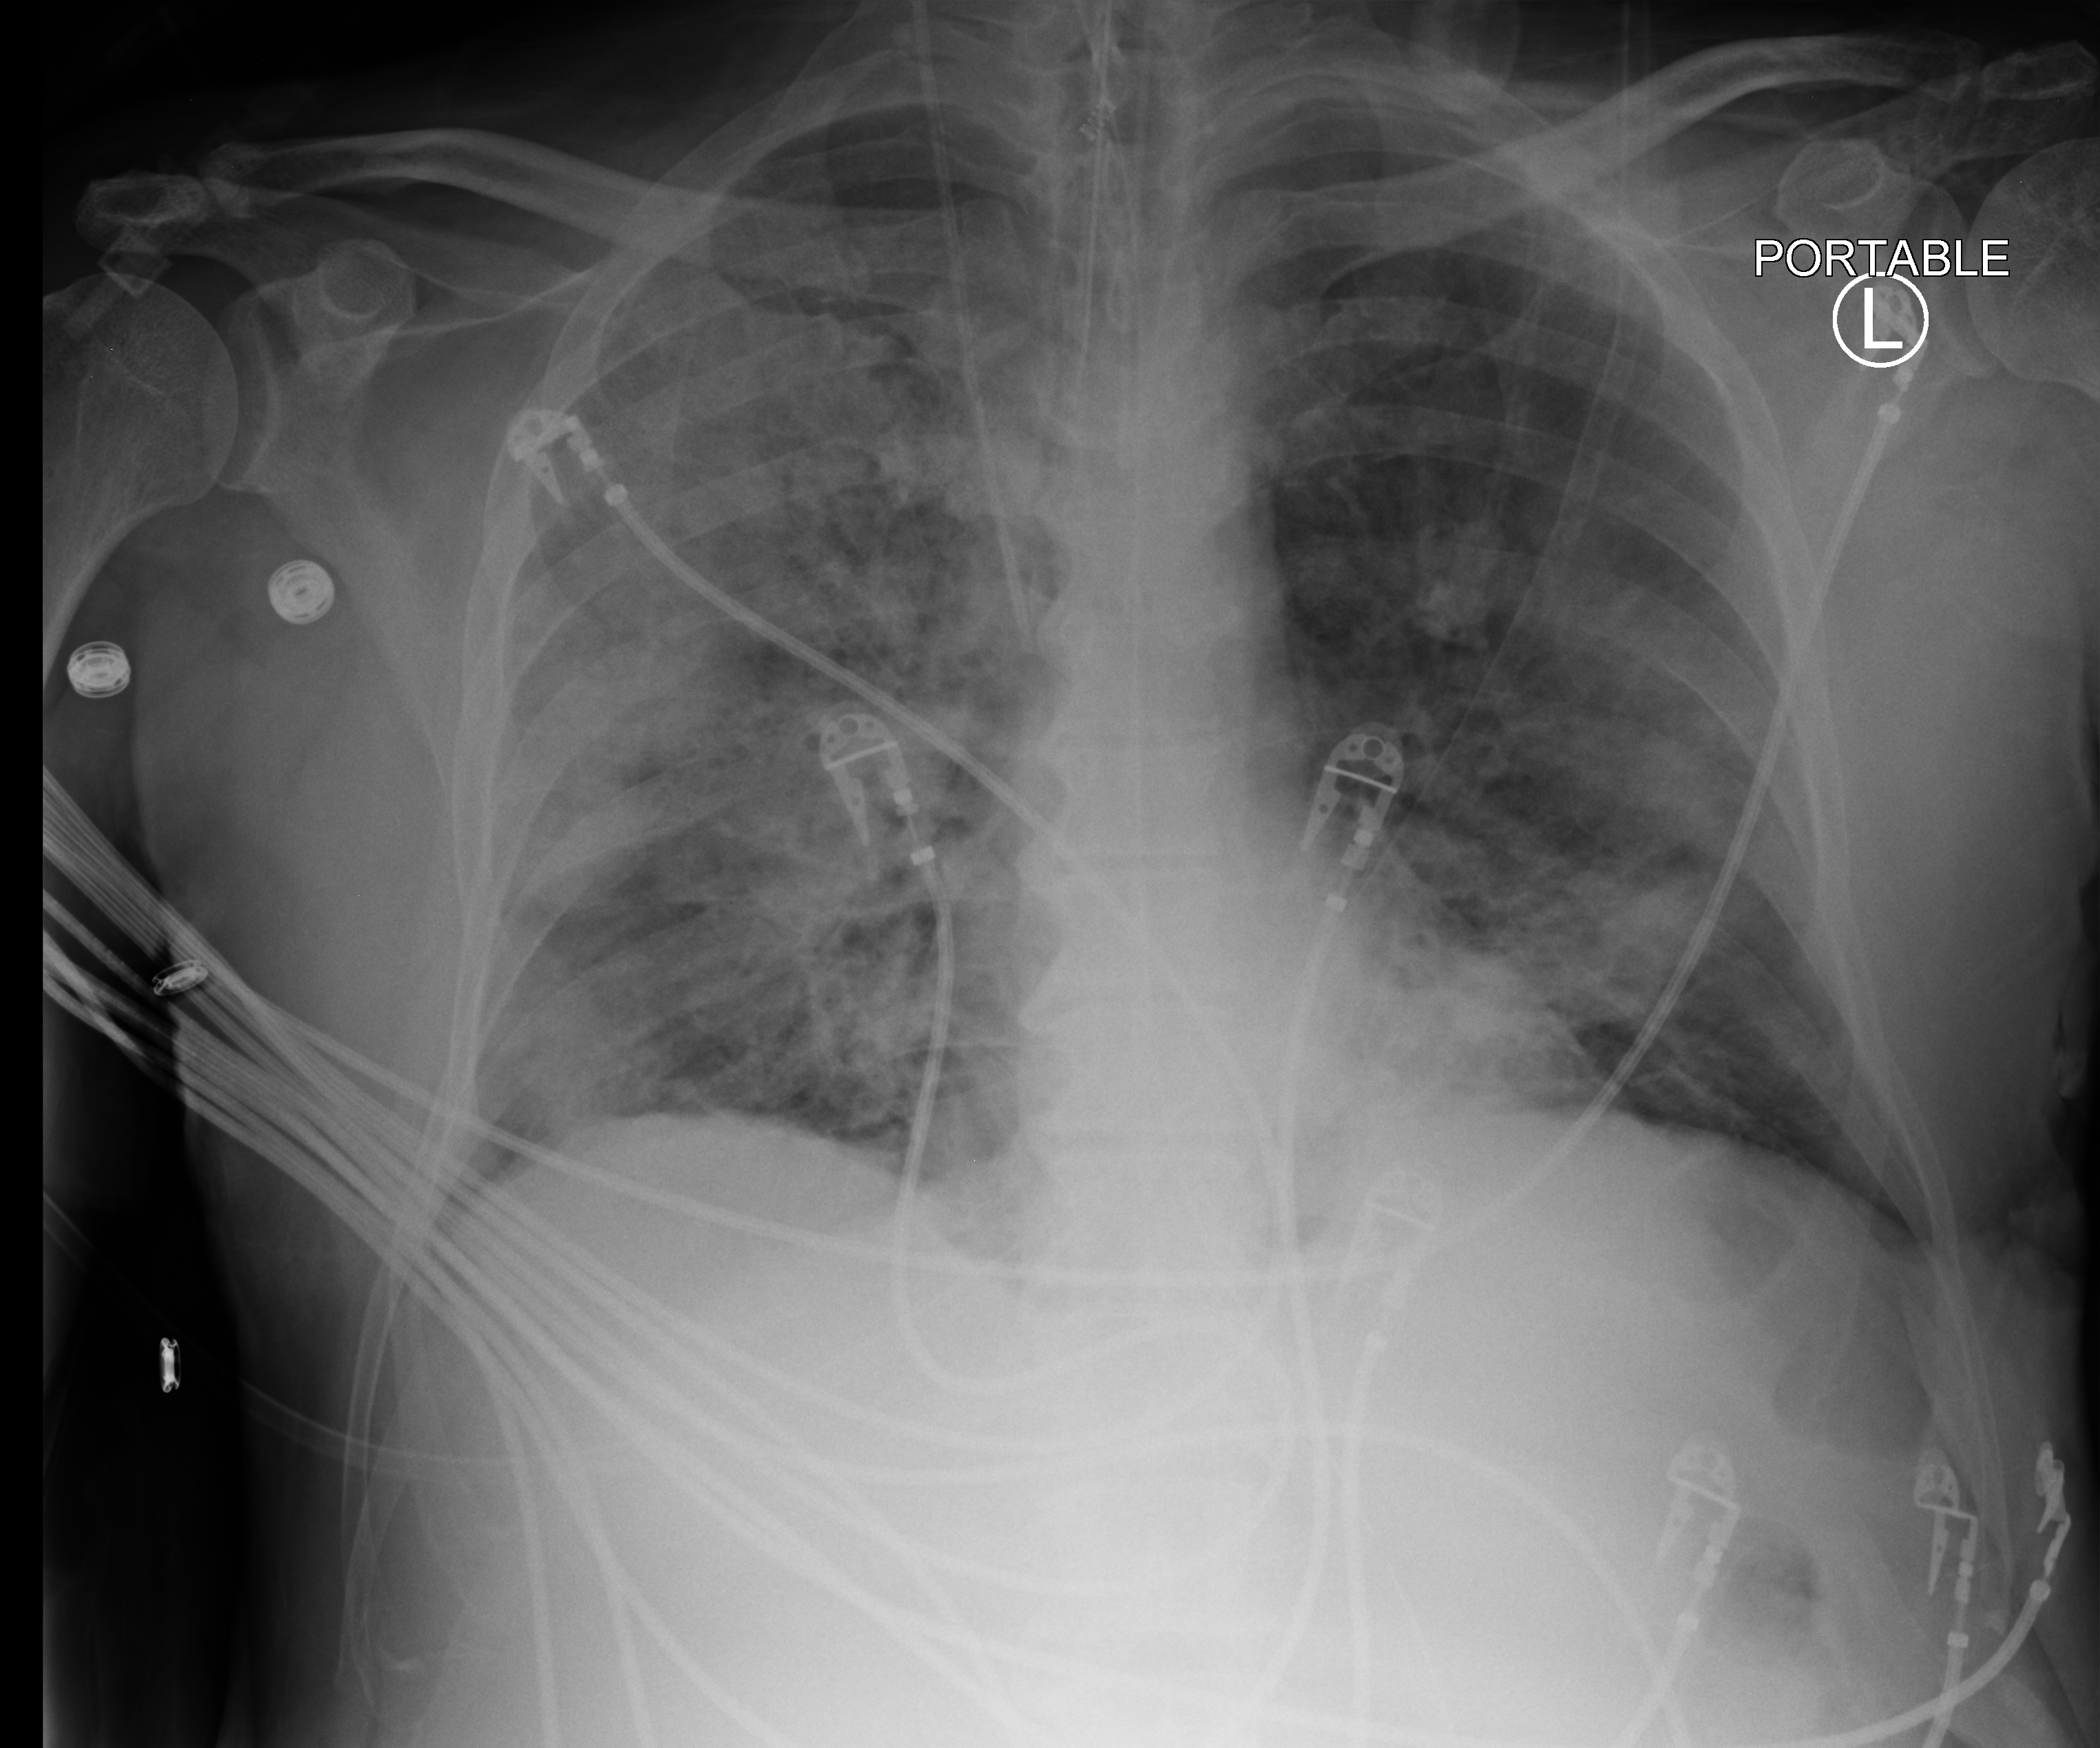
Bedside chest radiograph (computed radiography); anteroposterior (AP) projection. Patient hospitalised with COVID-19; male, aged 60–74 years.
Admission-level facts for this patient (not findings on this image; timing relative to this image not recorded): admitted to intensive care during this hospital stay: yes.